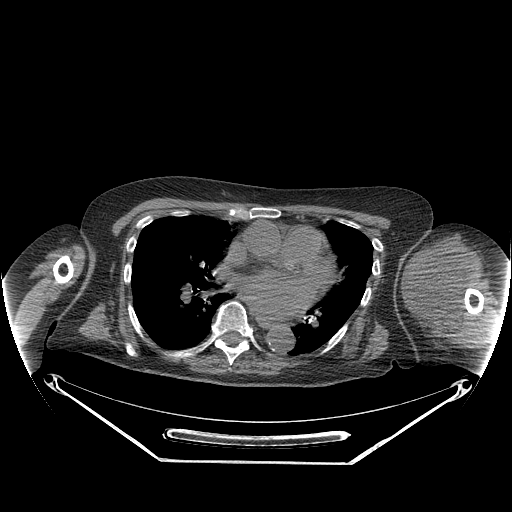
CT of an extremity soft-tissue mass (from a PET/CT study), one axial slice; position 173 of 267 along the scan axis; reconstruction kernel STANDARD; 140 kVp; soft-tissue window (W 400 / L 40 HU); 512 × 512 image matrix. Female patient. From the clinical record (not read from this slice): histological type: pleiomorphic leiomyosarcoma; grade: high; site of the primary tumour: left biceps.
Outlined on this slice (expert contour drawn on MRI and transferred to this co-registered scan by the dataset authors):
- gross tumour volume including surrounding oedema: box from (x=404, y=233) to (x=476, y=327) px
- gross tumour volume (mass): (x=404, y=235)–(x=471, y=321)